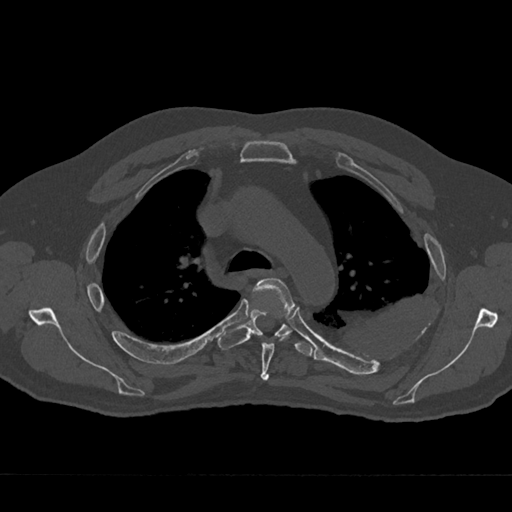
CT including the spine, one axial slice. Position 497 of 797 along the scan axis. Reconstruction kernel Br40s/3. 120 kVp. Bone window (W 1800 / L 400 HU). 0.5 mm slice thickness. 512 × 512 image matrix. Male patient, age 75 years. Case-level facts recorded for this patient, not image findings: primary cancer: renal; vertebrae with lytic lesions (as recorded): T4.
Structures marked on this image (semi-automatically segmented with operator editing):
- T4 vertebra: bounding box (x1, y1, x2, y2) in pixels: (253, 278, 295, 381)
- T5 vertebra: (218, 309, 313, 356)